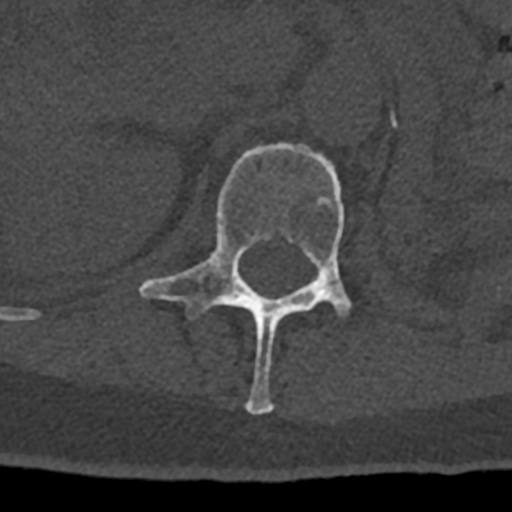
CT including the spine, one axial slice; slice 436 of 797 in the series (ordered by position); bone window (W 1800 / L 400 HU); 512 × 512 image matrix, field of view 160 × 160 mm. Male patient, age 74 years. From the clinical record (not read from this slice): primary cancer: renal; vertebrae with lytic lesions (as recorded): T10, L1, L2, L3, L4, L5.
Outlined on this slice (semi-automatically segmented with operator editing):
- L1 vertebra: bounding box [x1, y1, x2, y2] px = [139, 142, 352, 415]